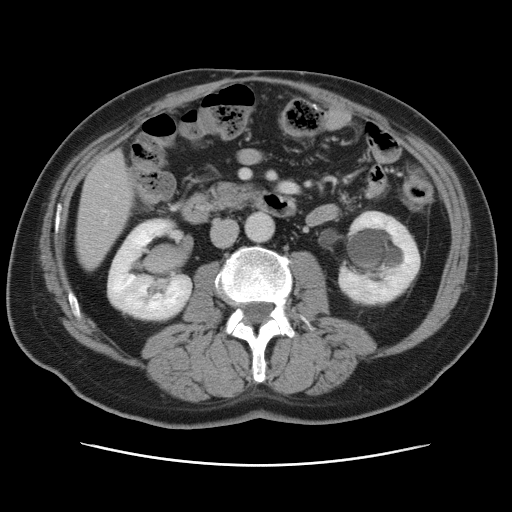
Contrast-enhanced abdominal CT, one axial slice; slice 21 of 80 in the series (ordered by position); 120 kVp; intravenous contrast given; soft-tissue window (W 400 / L 40 HU); 512 × 512 image matrix, field of view 370 × 370 mm. Male patient, age 69 years. From the clinical record (not read from this slice): diagnosis: colorectal cancer liver metastases, imaged before liver resection; multiple liver metastases: no; largest metastasis: 5 cm; chemotherapy before resection: no.
Outlined on this slice (outlined manually by an expert reader):
- hepatic veins: bounding box <104,186,107,212> (left, top, right, bottom; pixels)
- liver: <77,153,133,268>
- planned liver remnant (the part of the liver to remain after resection): <77,223,120,268>